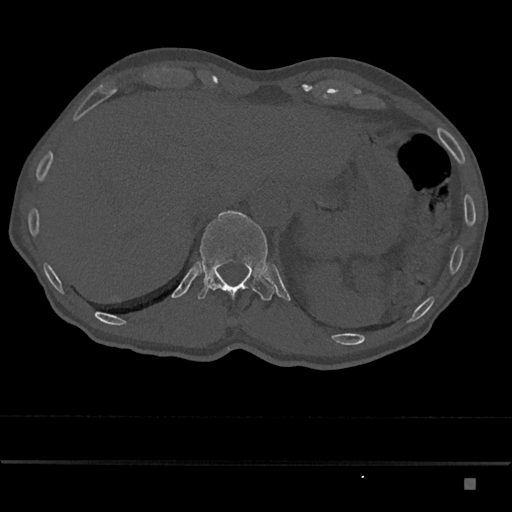
CT including the spine, one axial slice; slice 618 of 797 in the series (ordered by position); 120 kVp; bone window (W 1800 / L 400 HU); 0.5 mm slice thickness; 512 × 512 image matrix, field of view 390 × 390 mm. Male patient, age 72 years. From the clinical record (not read from this slice): primary cancer: prostate.
Annotated regions visible in this slice (semi-automatically segmented with operator editing):
- T12 vertebra: bounding box [x1, y1, x2, y2] px = [198, 211, 275, 301]